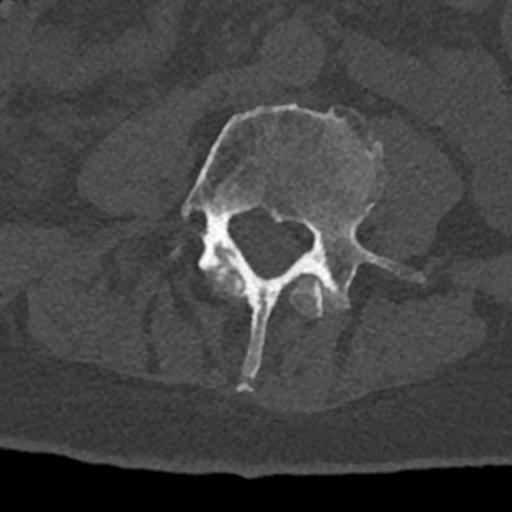
CT including the spine, one axial slice; slice 266 of 797 in the series (ordered by position); reconstruction kernel Br40s/3; bone window (W 1800 / L 400 HU); 0.5 mm slice thickness; 512 × 512 image matrix, field of view 160 × 160 mm. Male patient, age 74 years. From the clinical record (not read from this slice): primary cancer: renal.
Structures marked on this image (semi-automatic segmentation, software-assisted and operator-edited):
- L3 vertebra: bounding box <209,267,332,317> (left, top, right, bottom; pixels)
- L4 vertebra: <182,103,424,391>